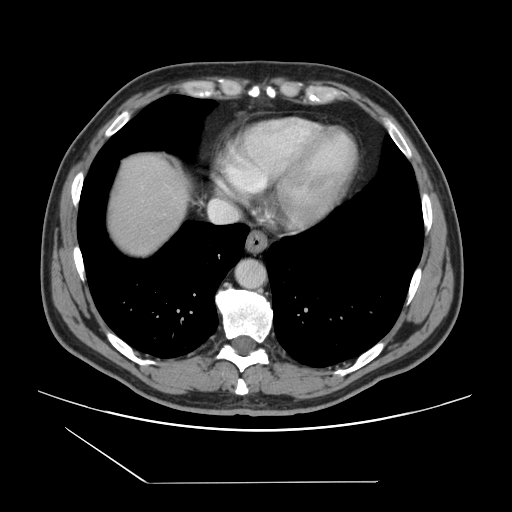
Contrast-enhanced abdominal CT, one axial slice. Slice 135 of 157 in the series (ordered by position). Soft-tissue window (W 400 / L 40 HU). 2.5 mm slice thickness. 512 × 512 image matrix. Male patient, age 61 years. From the clinical record (not read from this slice): diagnosis: colorectal cancer liver metastases, imaged before liver resection; multiple liver metastases: yes; largest metastasis: 5.5 cm; chemotherapy before resection: no.
Outlined on this slice (manually delineated by an expert):
- liver: bounding box [x1, y1, x2, y2] px = [110, 157, 188, 252]
- planned liver remnant (the part of the liver to remain after resection): [110, 157, 188, 231]
- liver metastasis: [141, 252, 150, 257]